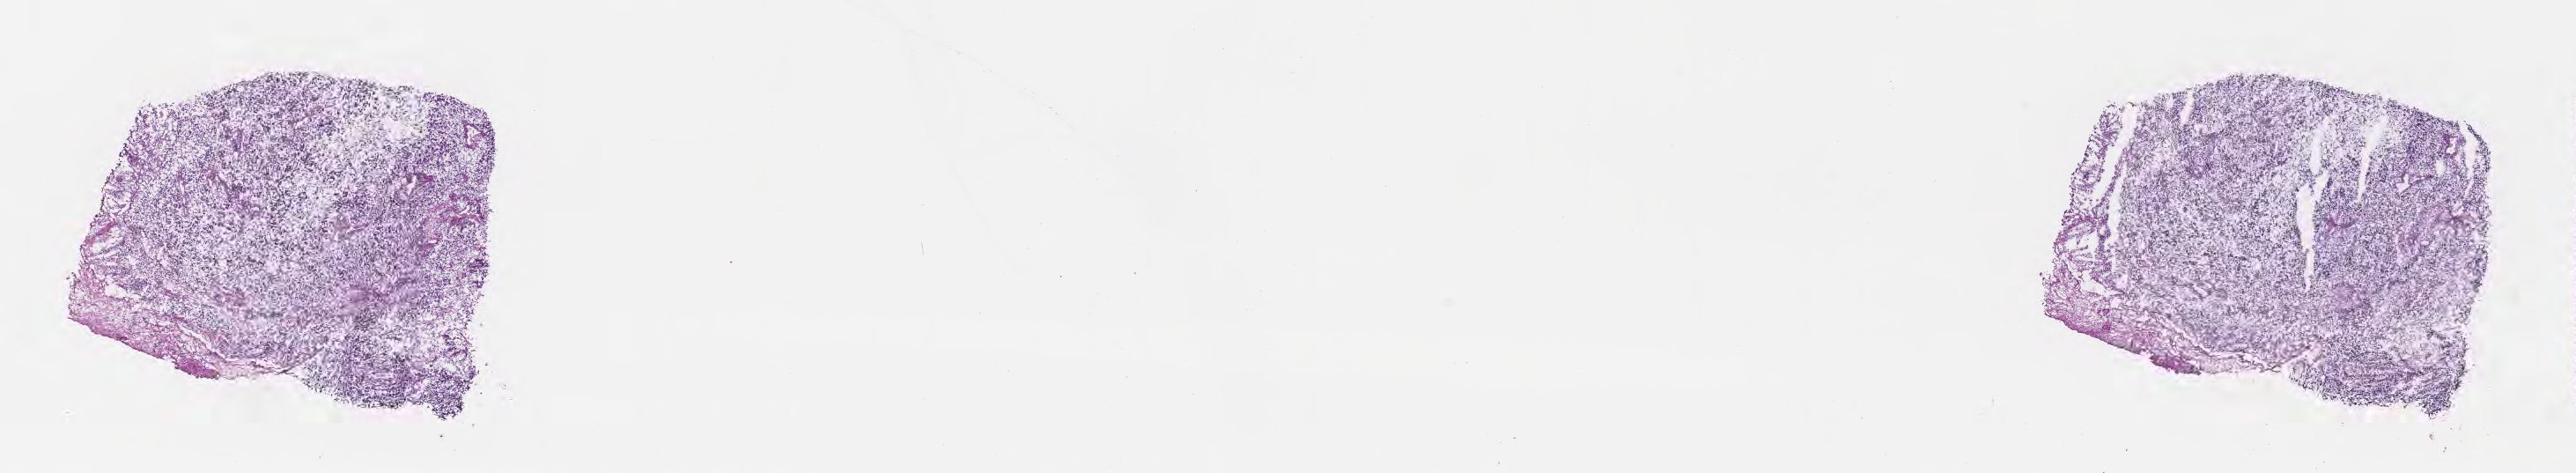
Whole-slide image, hematoxylin and eosin (H&E) stain, whole scanned area (about 23.6 x 4.3 mm) shown as a low-resolution overview; frozen section (tissue freezing medium); specimen: primary tumor; anatomic site: brain. Male patient; age at initial diagnosis 51 years. Composition of this section per pathologist review: tumor cells 73%, tumor nuclei 83%, stromal cells 10%, necrosis 2%, normal cells 15%. Infiltration values recorded for this section: lymphocyte infiltration 0%, monocyte infiltration 0%, neutrophil infiltration 0%.
* histologic diagnosis: Glioblastoma, NOS